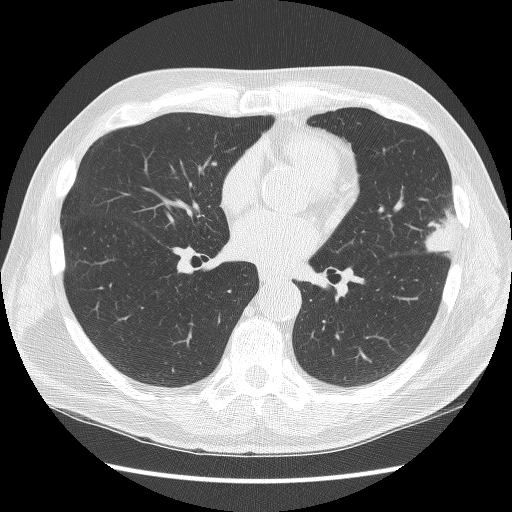
Chest CT (low-dose screening protocol), one axial image, third annual screen, lung window (W 1500 / L -600 HU), 2.5 mm slice thickness, lung (sharp) reconstruction kernel (BONE), slice 67 of 134 in the series, 512 × 512 image matrix, field of view 350 × 350 mm. Male participant, aged 67 years at enrolment.
Expert reader's lesion annotation, box from (x=408, y=199) to (x=473, y=271) px. Screening reader's record for this exam (one nodule recorded; not confirmed to be the boxed lesion): non-calcified nodule or mass ≥4 mm, left upper lobe, 22 × 17 mm, poorly defined margins, soft tissue attenuation, pre-existing on the prior screen: yes; interval growth: yes. Lung cancer was diagnosed 72 days after this screen: squamous cell carcinoma, NOS, left upper lobe, moderately differentiated (G2), stage IB (AJCC 6th edition), 25 mm at pathology.